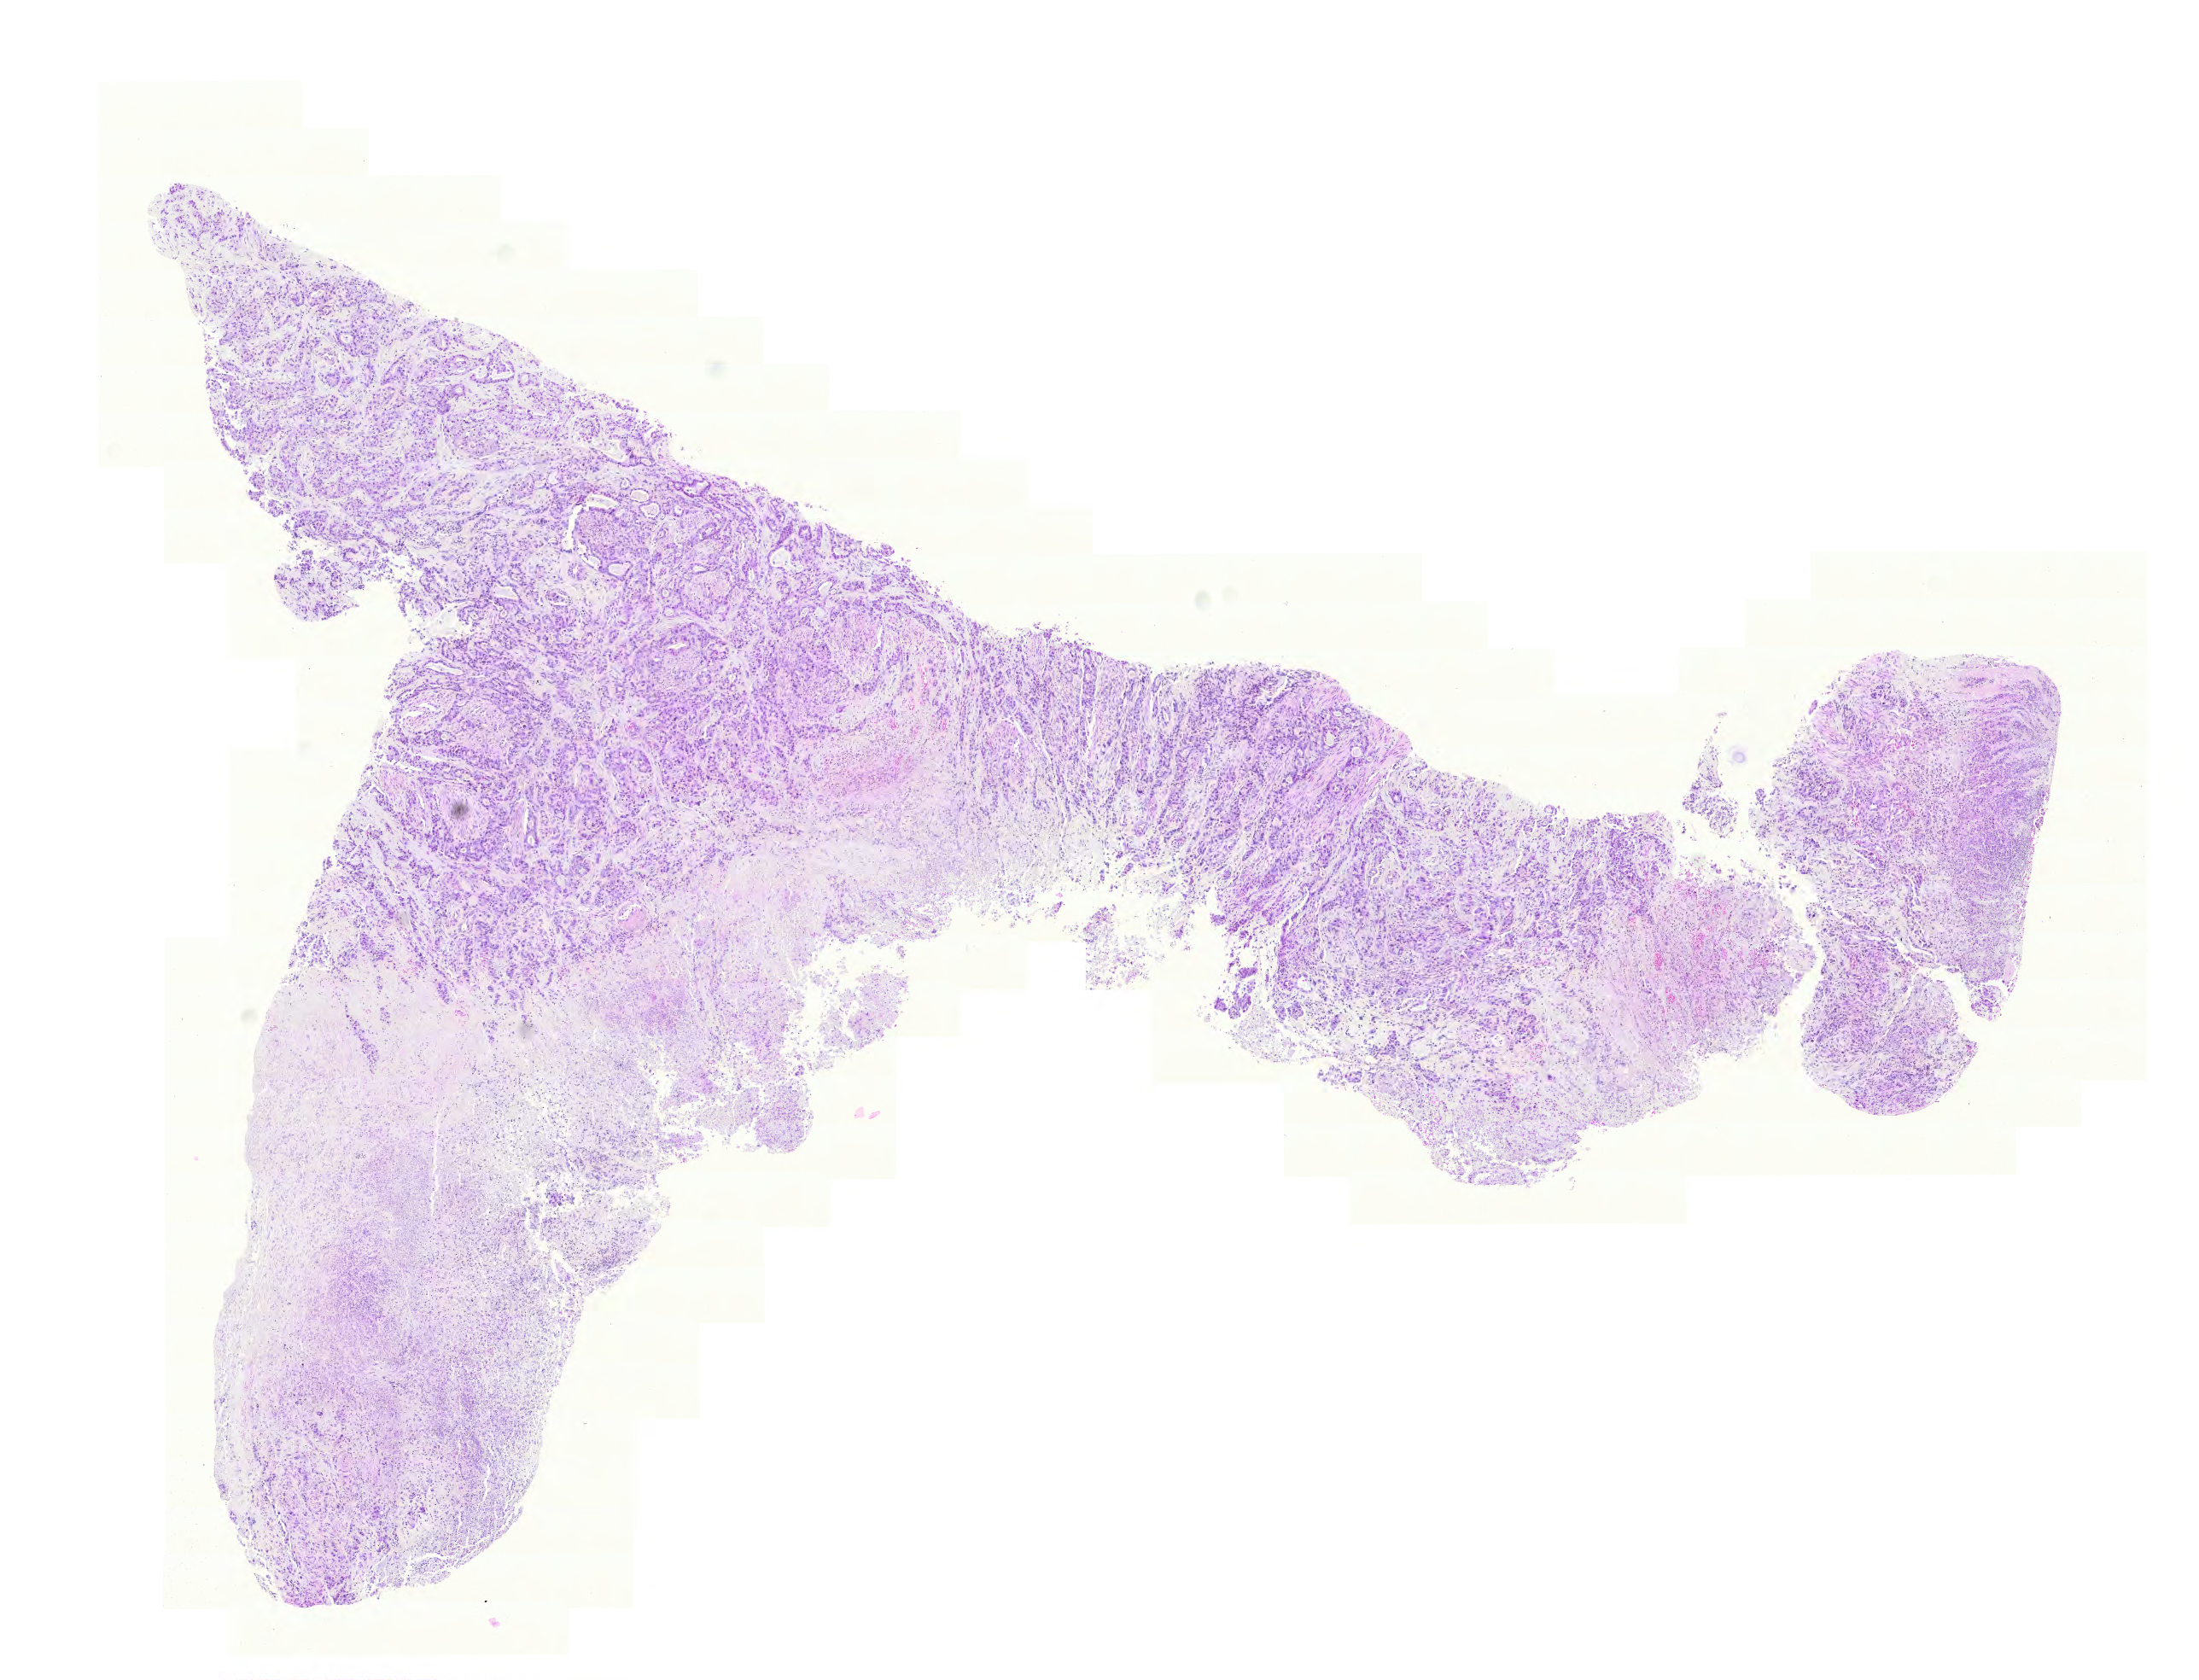
Whole-slide histology image, Hematoxylin and eosin (H&E) stained, whole scanned area (about 9.6 x 7.3 mm, from a 20x scan) shown as a low-resolution overview. FFPE section. Sample: primary tumour, stomach. Patient: female, age at initial diagnosis 75 years. Histologic grade: G3 (poorly differentiated).
Pathologic diagnosis: Adenocarcinoma, NOS (cardia, NOS). AJCC pathologic stage: IV (5th edition). TNM: T4 N1 M1.